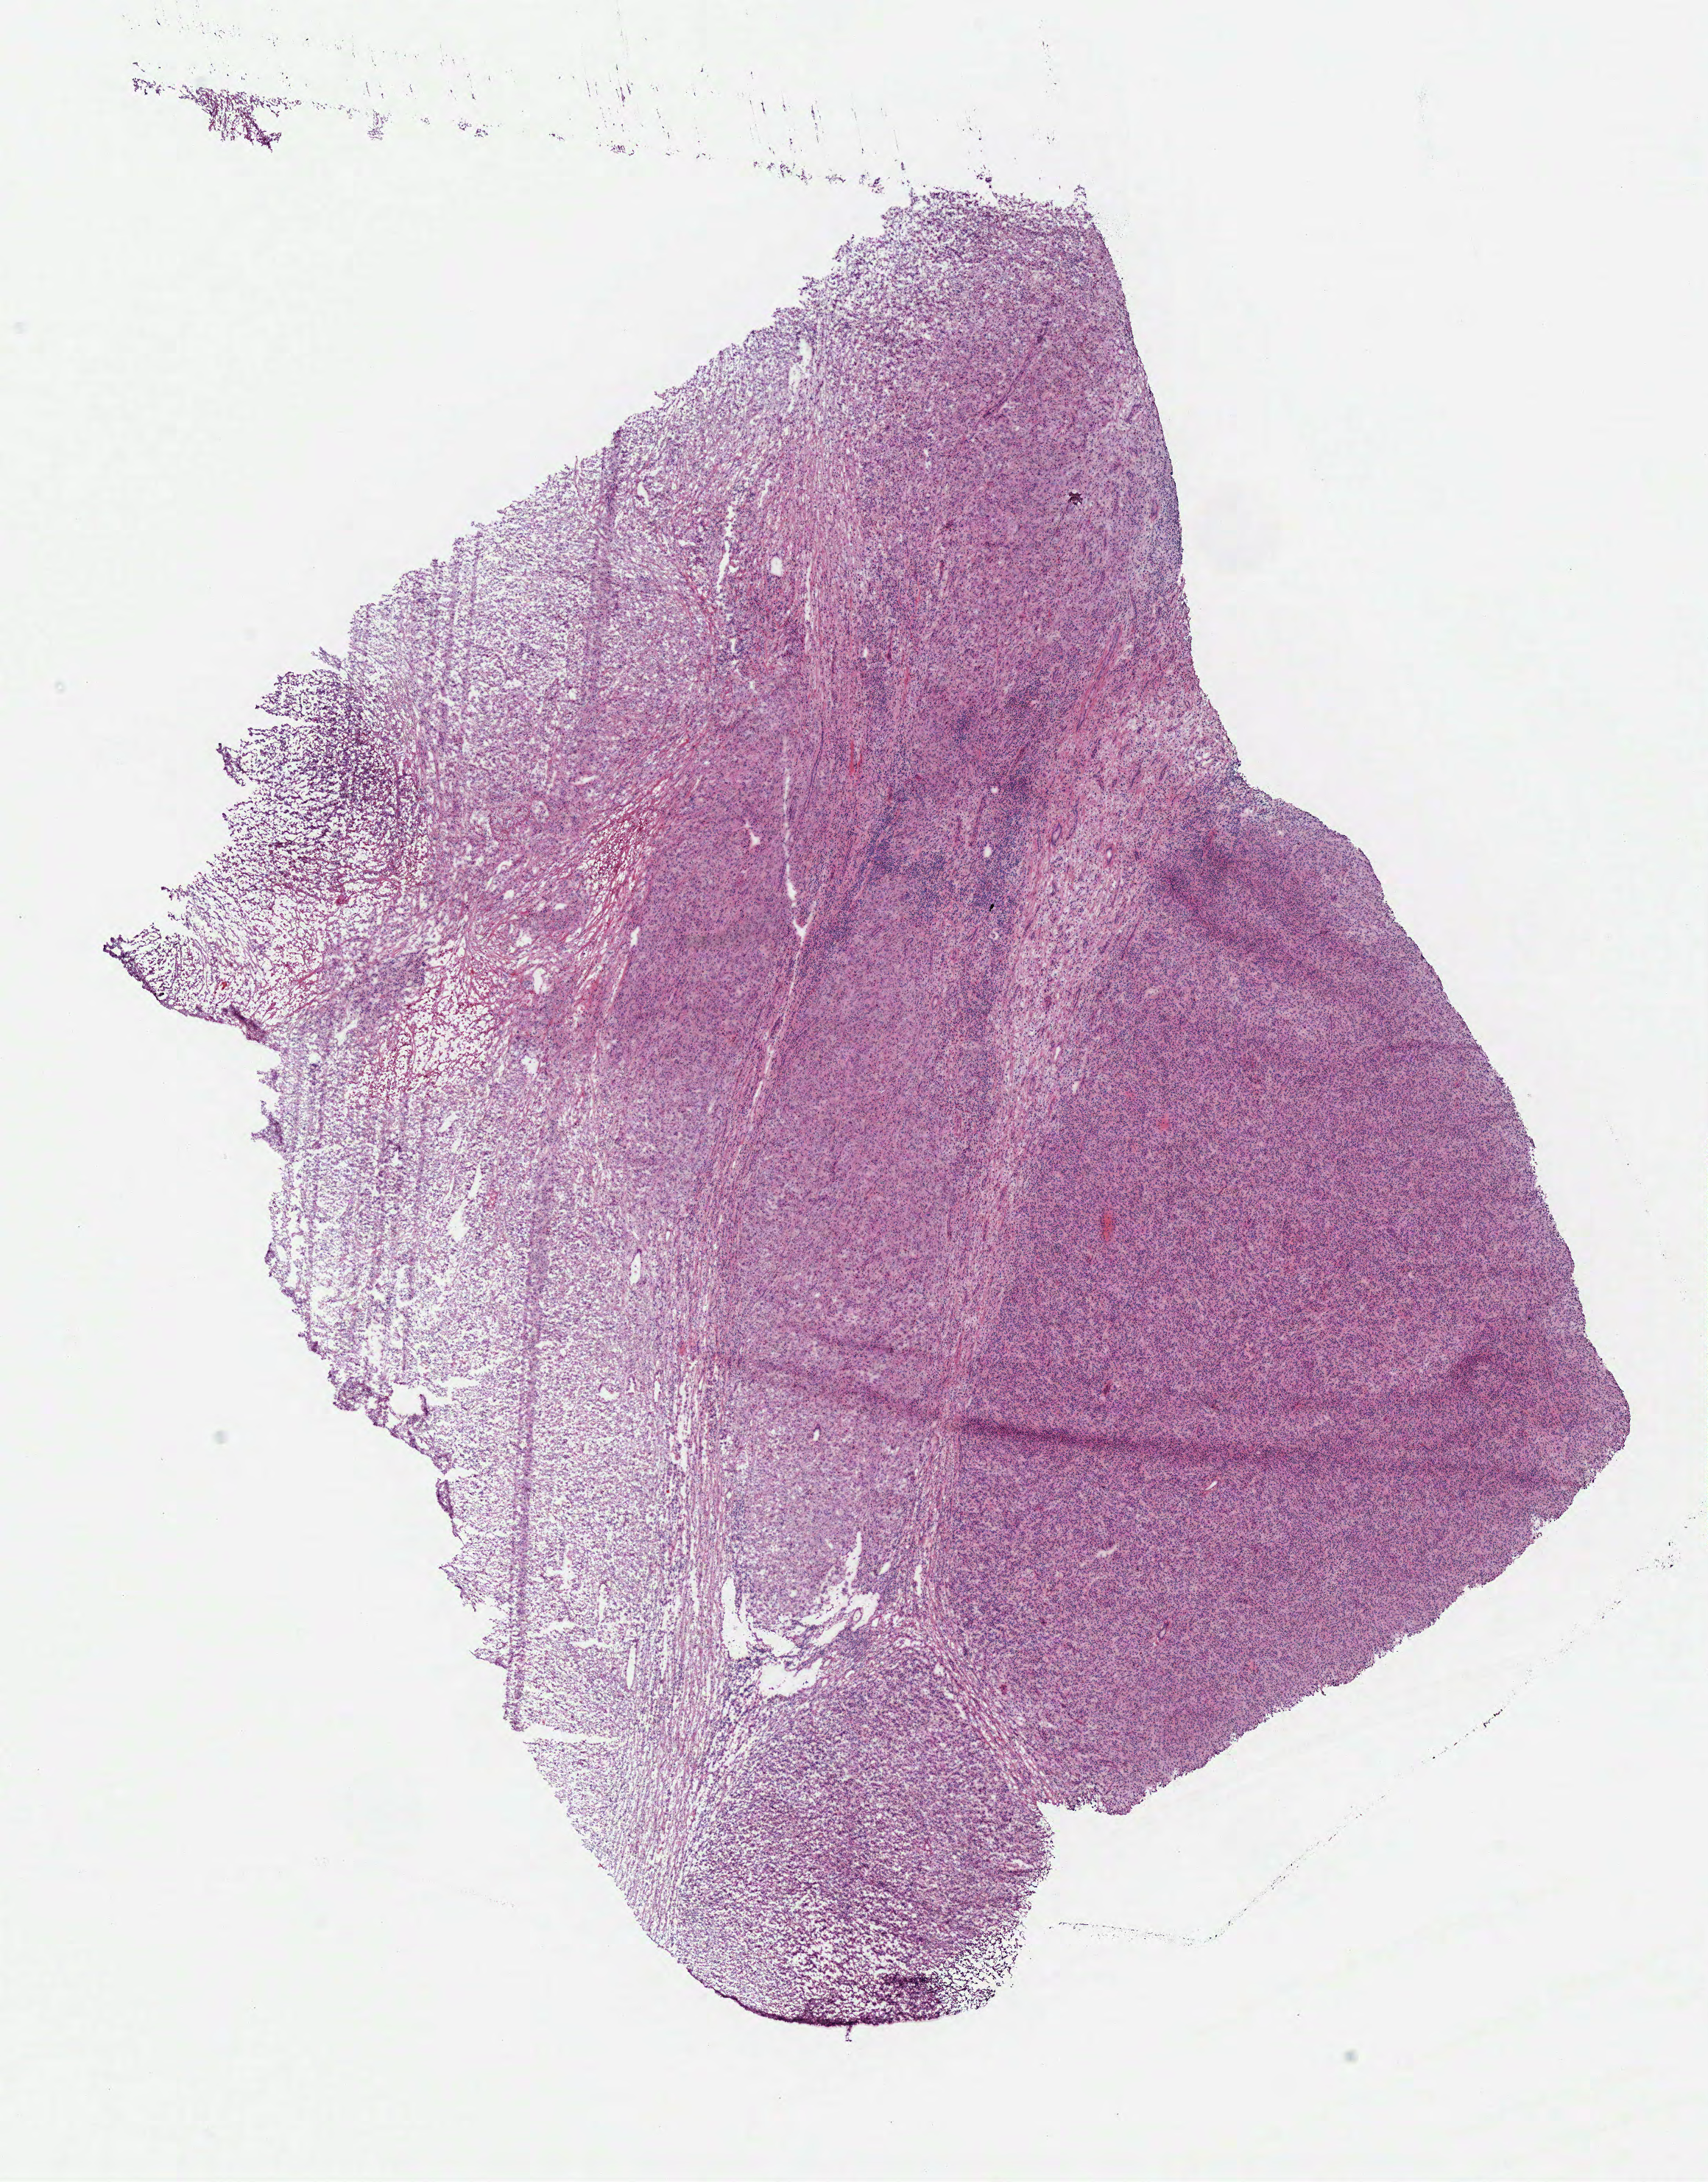
Hematoxylin and eosin (H&E) stained whole-slide image — low-resolution overview of the scanned area, about 9.1 x 11.7 mm, frozen section from the top of the tissue portion, kidney, primary tumour sample. Male patient; age at initial diagnosis 61 years. Histologic grade: G4 (undifferentiated). Slide review estimates, as recorded: tumour cells 82%, tumour nuclei 80%, normal cells 0%, stromal cells 15%, necrosis 3%.
AJCC pathologic stage: IV. Laterality: right. Pathologic diagnosis: Clear cell adenocarcinoma, NOS. Lymph nodes positive (case pathology): 1 of 2 examined.